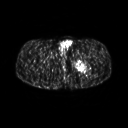
FDG PET of an extremity soft-tissue mass (from a PET/CT study), one axial slice; slice 257 of 267 in the series (ordered by position); 3.27 mm slice thickness; 128 × 128 image matrix, field of view 500 × 500 mm. Male patient, age 27 years. From the clinical record (not read from this slice): histological type: extraskeletal osteosarcoma; grade: high; site of the primary tumour: left adductur.
Outlined on this slice (expert contour drawn on MRI and transferred to this co-registered scan by the dataset authors):
- gross tumour volume (mass): bounding box <72,52,95,75> (left, top, right, bottom; pixels)